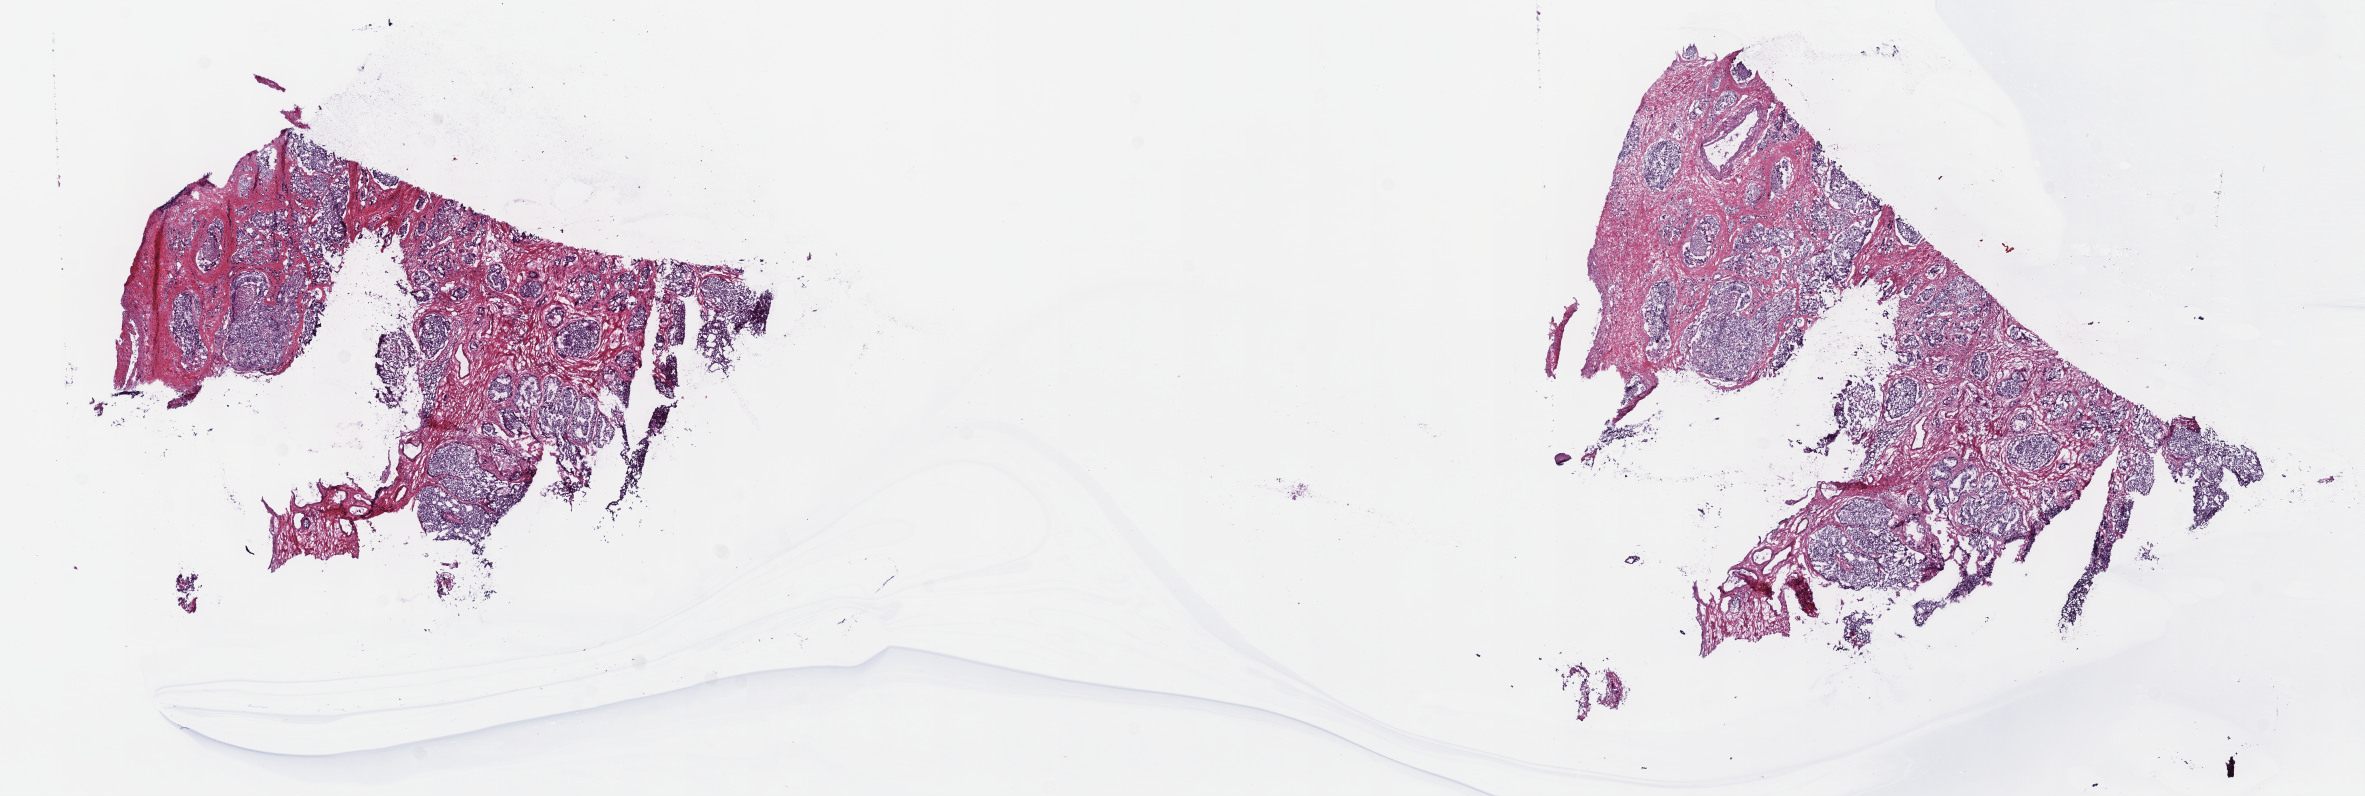
Digitized Hematoxylin and eosin (H&E) stained tissue section (whole slide) — whole scanned area (about 19.1 x 6.4 mm, slide scanned at 40x) shown as a low-resolution overview; frozen section; primary tumour sample from the prostate. Patient: male, age at initial diagnosis 69 years. Gleason score: 9 (4+5). Composition of this section per pathologist review: tumour cells 70%, tumour nuclei 70%, normal cells 5%, stromal cells 25%, necrosis 0%. Inflammatory infiltration, as recorded: lymphocyte infiltration 40%, monocyte infiltration 20%, neutrophil infiltration 20%.
Lymph nodes positive (case pathology): 3 of 19 examined. Pathologic diagnosis: Adenocarcinoma, NOS (prostate gland).